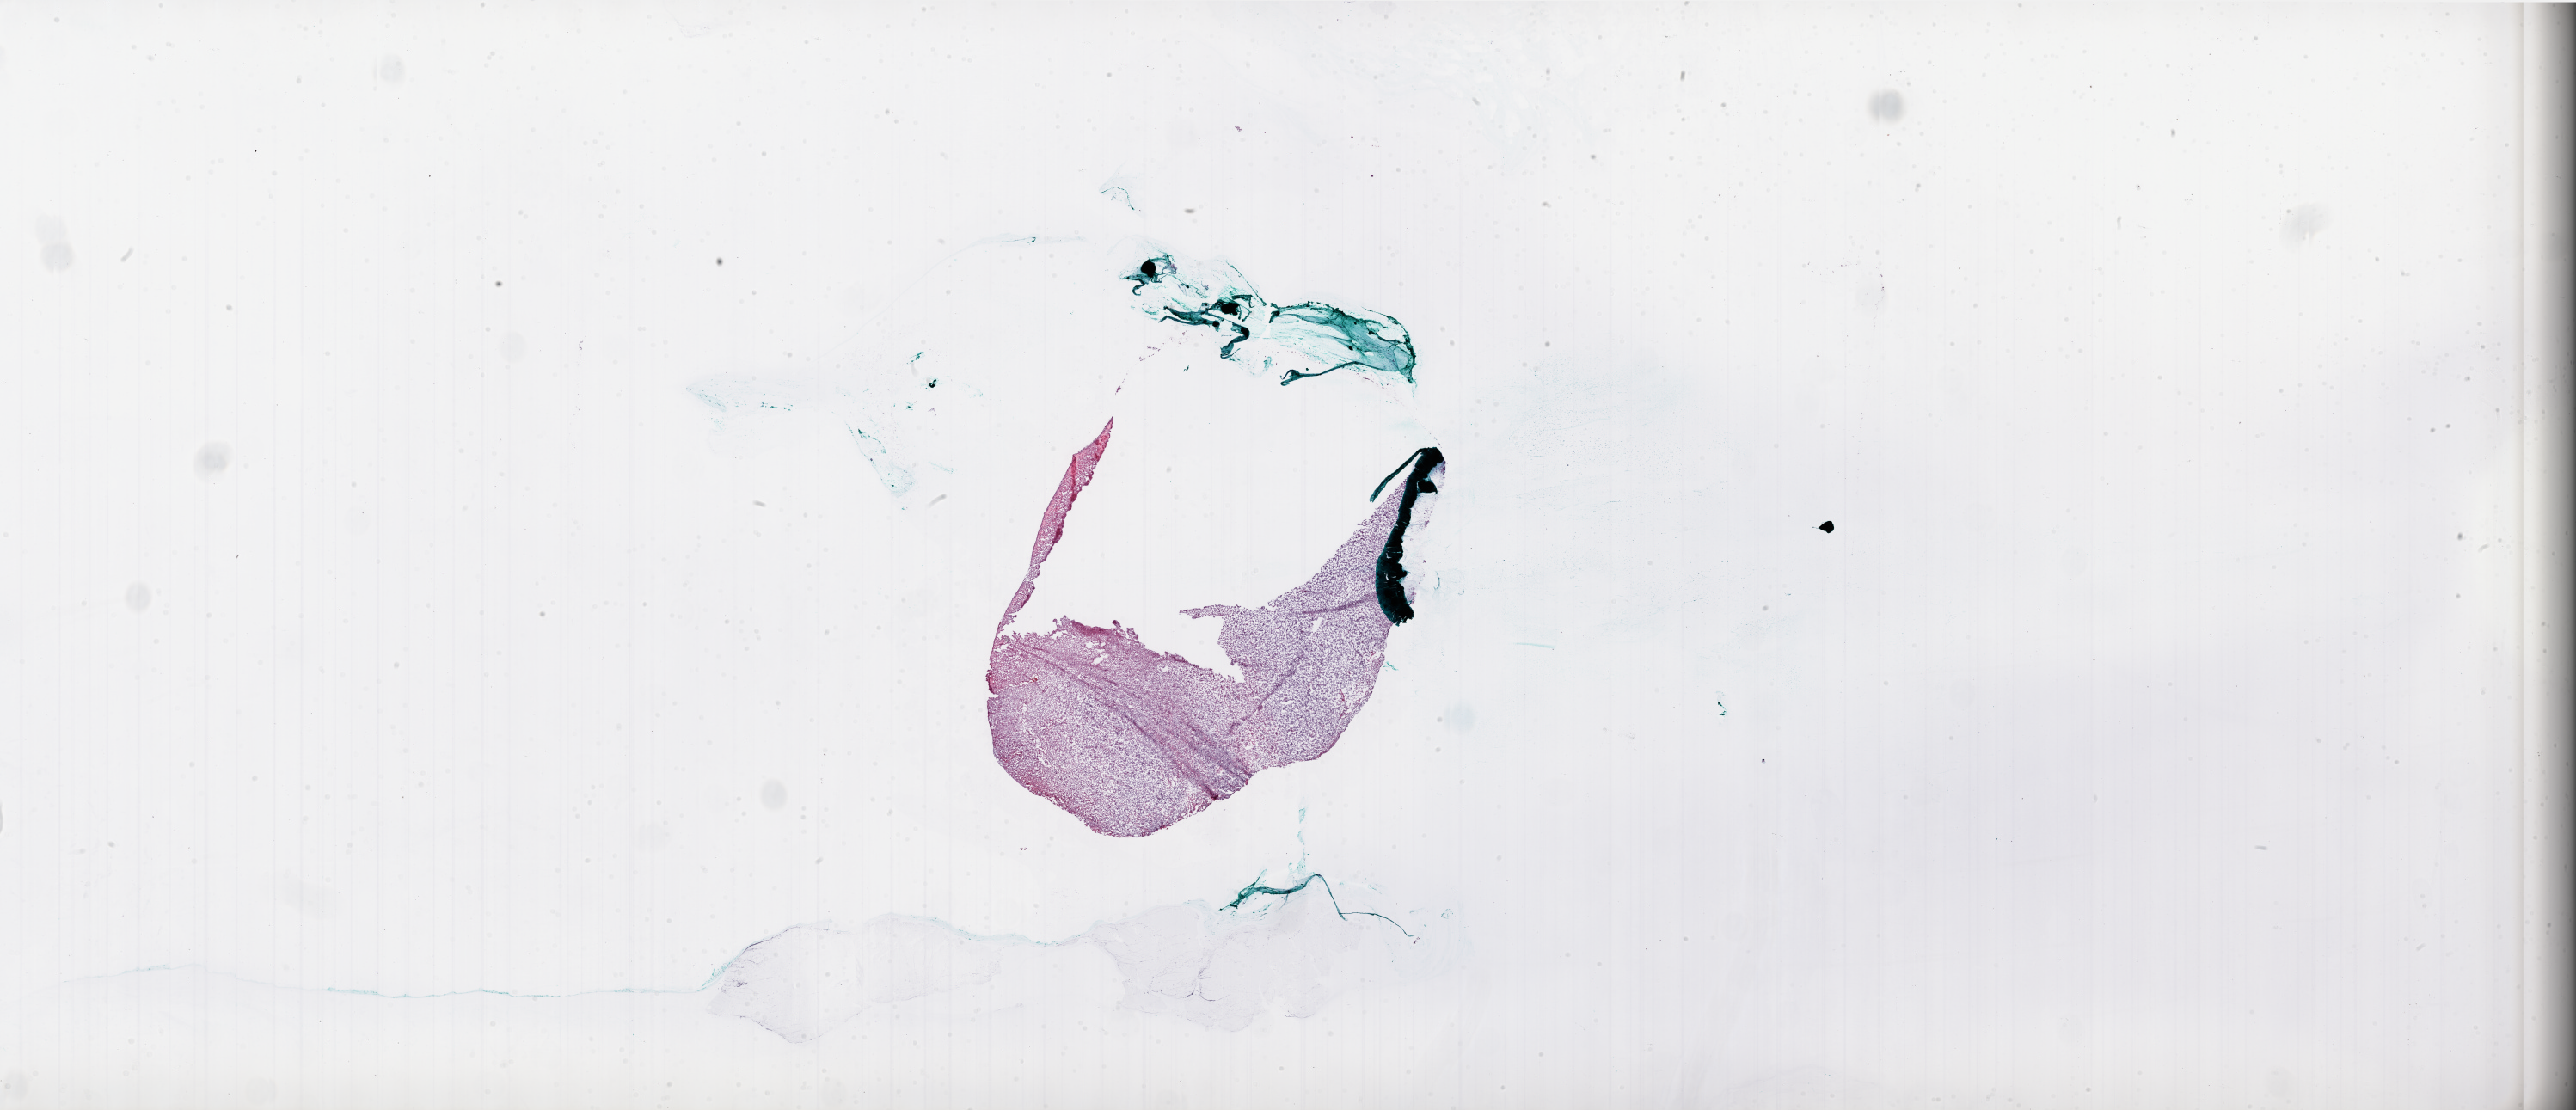
Whole-slide histology image, Hematoxylin and eosin (H&E) stained — low-resolution overview of the scanned area, about 48.0 x 20.7 mm, frozen section from the bottom of the tissue portion, sample: primary tumour, brain. Male, age 36 years at initial diagnosis. Pathologist review of this section (percent, as recorded): tumour cells 70%, tumour nuclei 95%, normal cells 0%, stromal cells 25%, necrosis 5%. Infiltration values recorded for this section: lymphocyte infiltration 0%.
Histologic diagnosis: Glioblastoma.